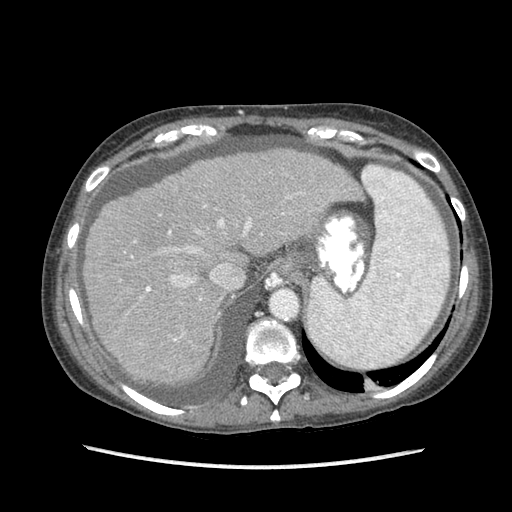
Contrast-enhanced abdominal CT (liver protocol), one axial slice; slice 69 of 87 in the series (ordered by position); 120 kVp; soft-tissue window (W 400 / L 40 HU); 512 × 512 image matrix, field of view 340 × 340 mm. Case-level facts recorded for this patient, not image findings: diagnosis: hepatocellular carcinoma (patient treated with transarterial chemoembolisation; whether this scan precedes or follows treatment is not stated here); TNM stage (as recorded): Stage-IIIB; Child-Pugh class: A.
Outlined on this slice (semi-automatically segmented with operator editing):
- liver parenchyma outside the tumour (the mass and vessels are separate outlines, so this box may not span the whole liver): bounding box (x1, y1, x2, y2) in pixels: (84, 148, 360, 382)
- liver vessels: (131, 192, 300, 341)